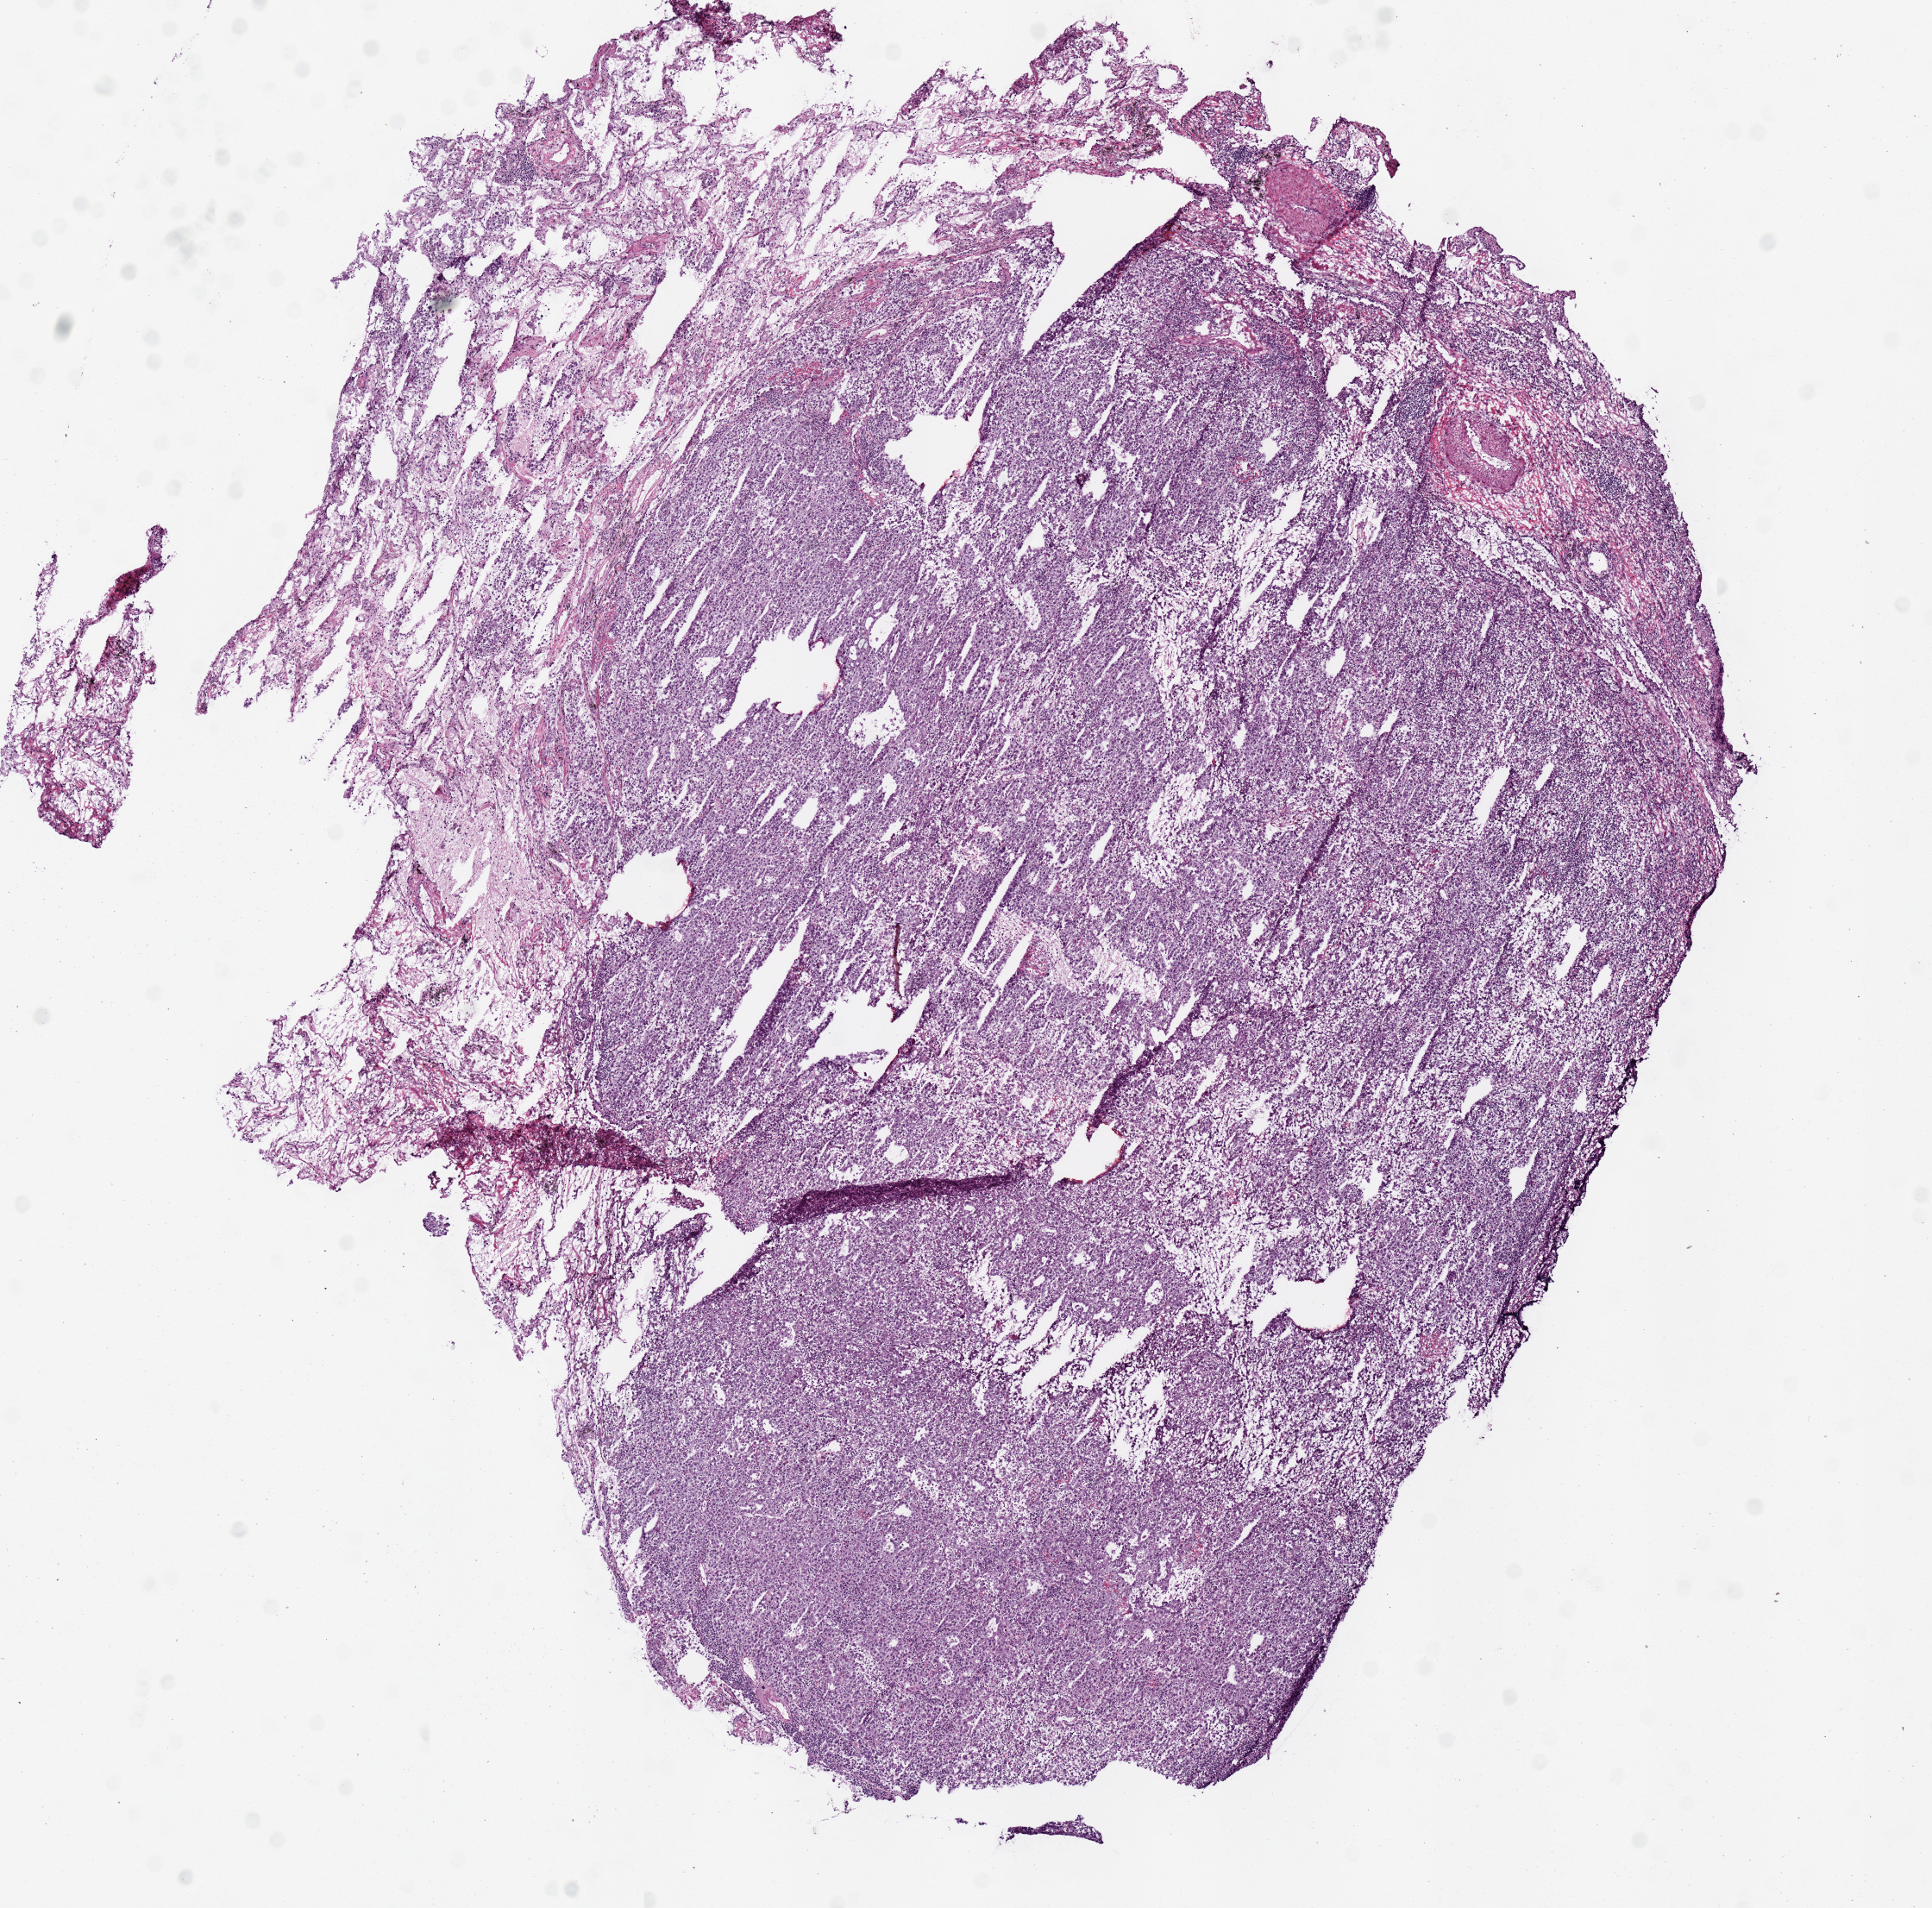
Digitized H&E-stained tissue section (whole slide), low-resolution overview of the scanned area, about 8.9 x 8.7 mm (acquisition: 20x scan), frozen section from the top of the tissue portion, lung, primary tumour sample. Patient: male, age at initial diagnosis 71 years. Composition of this section per pathologist review: tumour cells 90%, tumour nuclei 60%, normal cells 0%, stromal cells 10%, necrosis 0%.
• laterality: right
• TNM: T1a N0 M0
• pathologic diagnosis: Solid carcinoma, NOS (upper lobe, lung)
• AJCC pathologic stage: IA